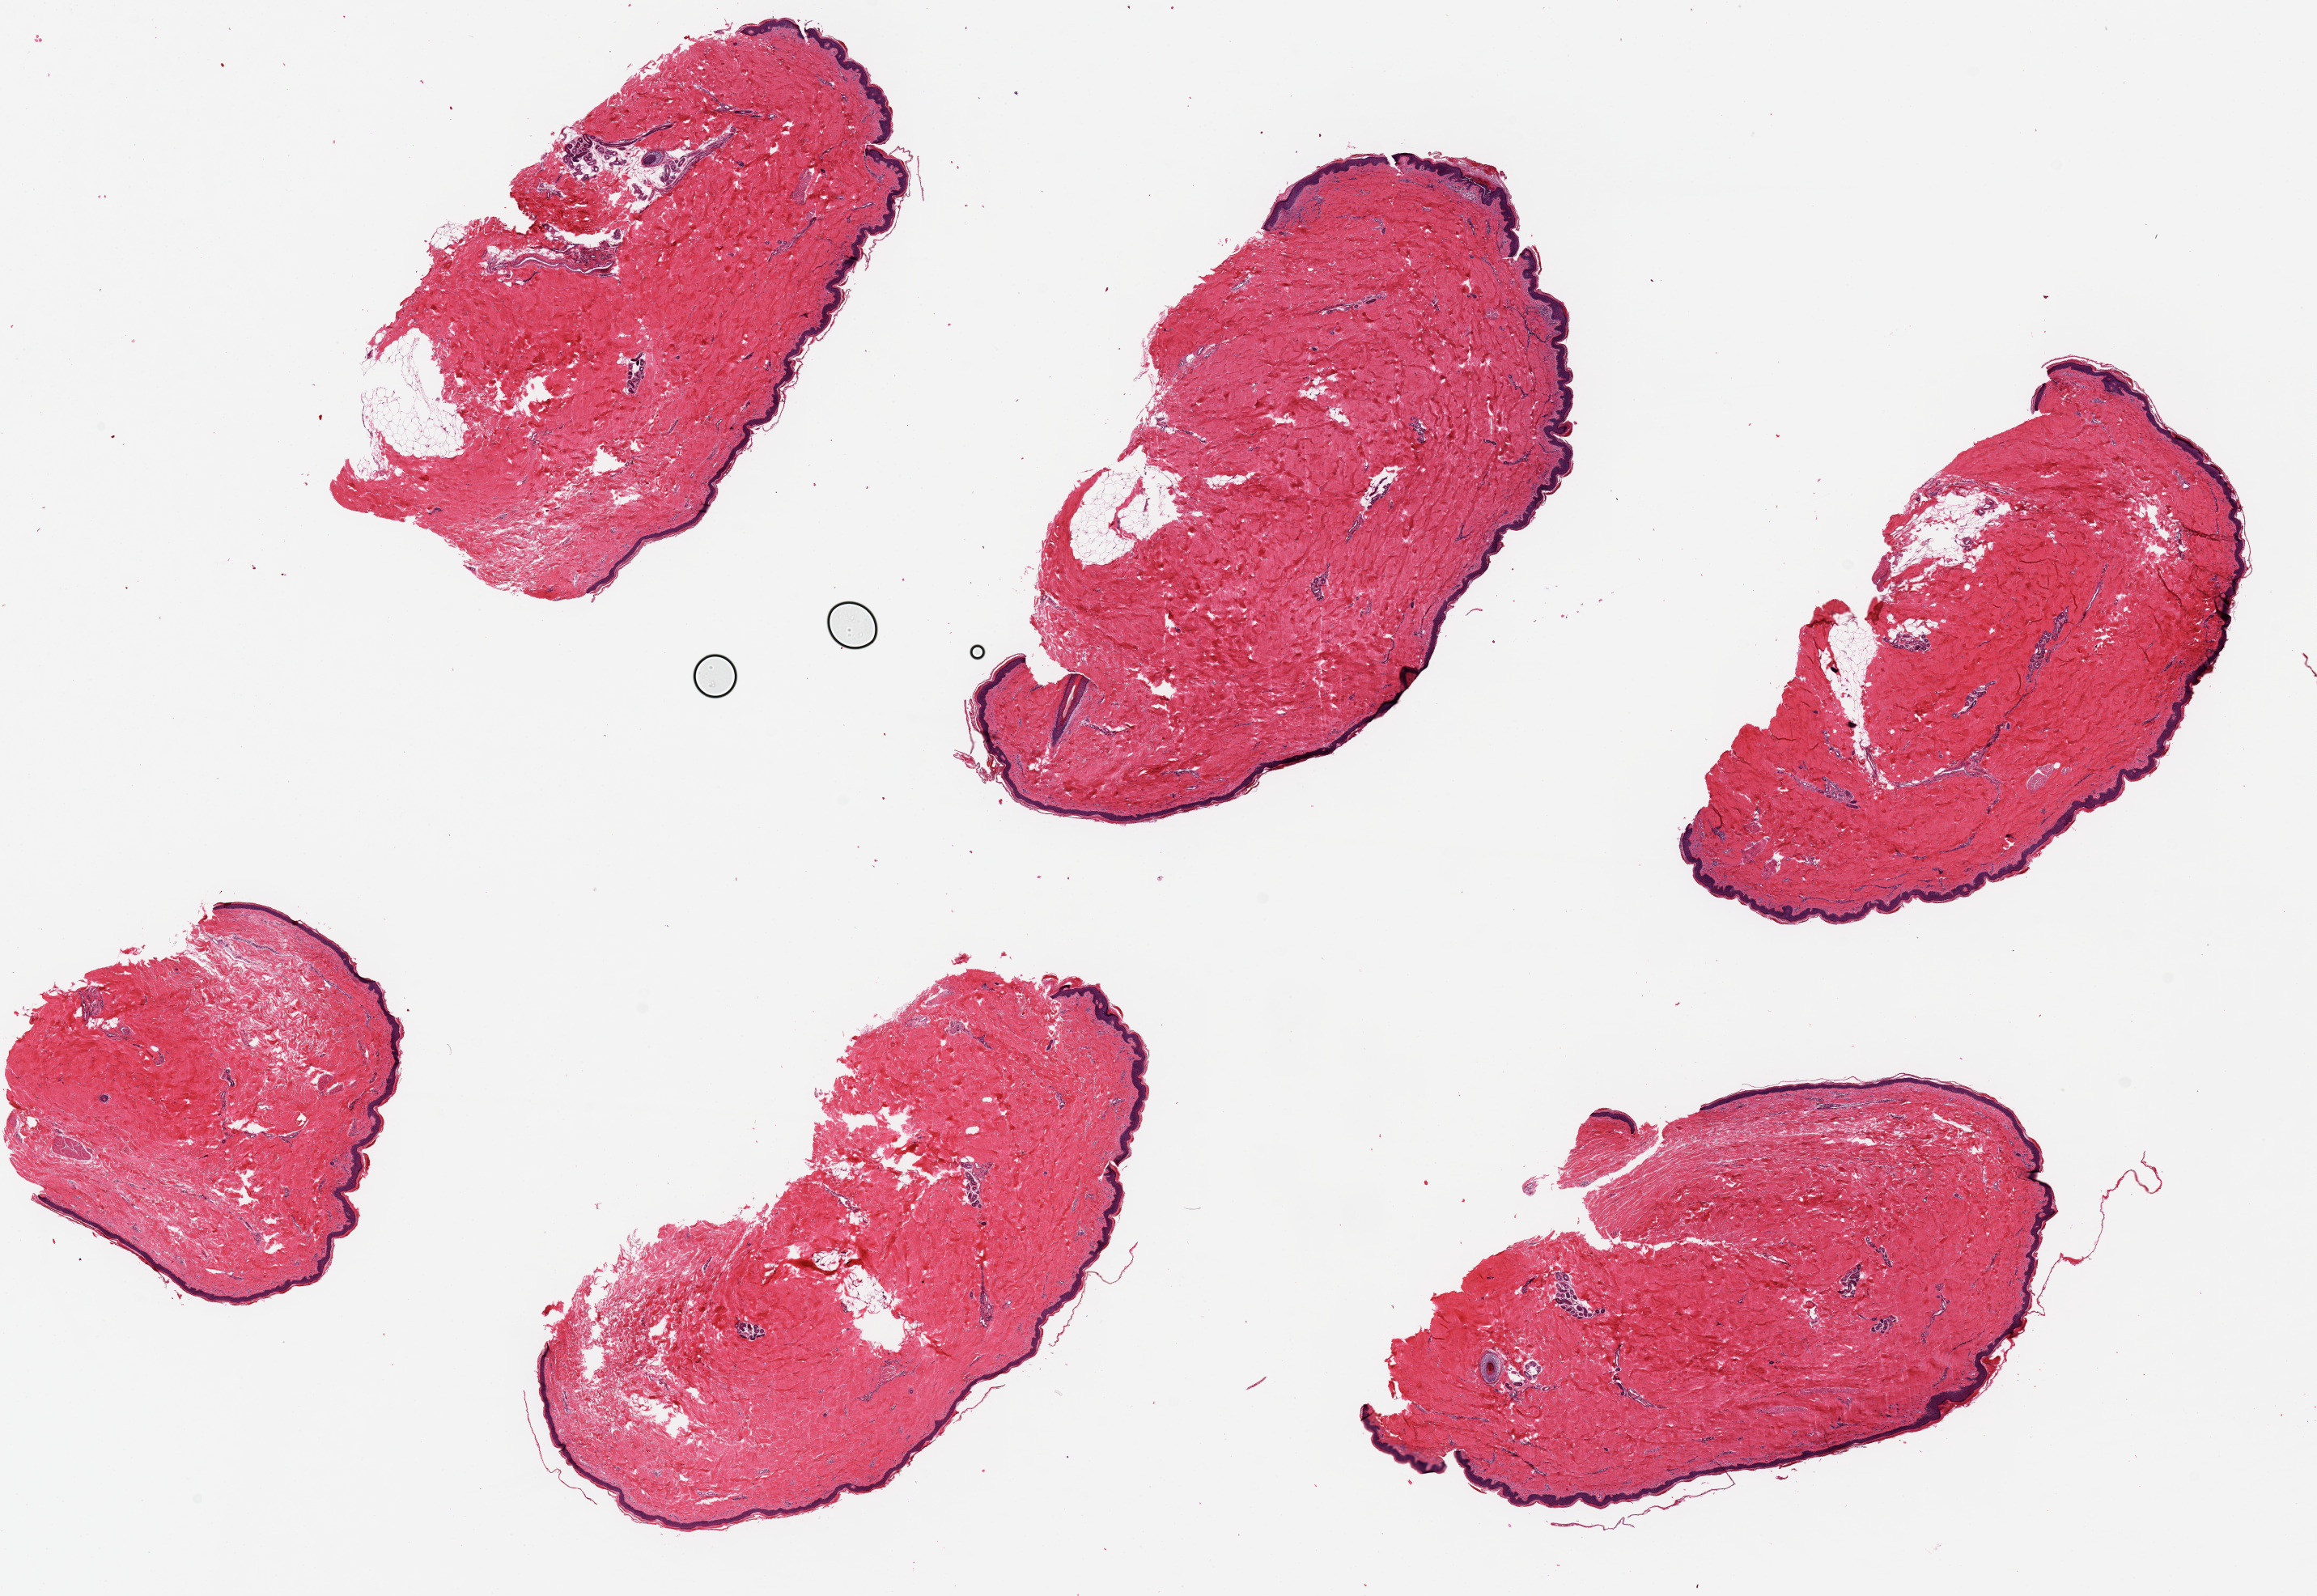
Digitized H&E-stained section — a low-resolution overview of the entire scanned area, about 22.6 x 15.6 mm (from a 20x scan); PAXgene-fixed, paraffin-embedded tissue; section of skin of suprapubic region (target tissue); tissue donor sample. Female donor.
Reviewer comment on this tissue sample: 6 pieces, up to 9.5x4mm; 1-2% thickness is squamous epithelium.